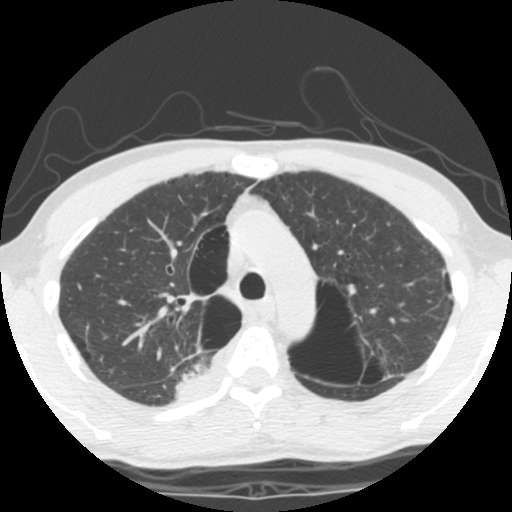
Low-dose screening chest CT, one axial slice; reconstruction kernel STANDARD; 140 kVp; lung window (W 1500 / L -600 HU); 512 × 512 image matrix, field of view 295 × 295 mm.
Structures marked on this image (expert manual segmentation):
- lesion 1 (tumor, upper lobe of right lung): bounding box <176,365,224,405> (left, top, right, bottom; pixels)